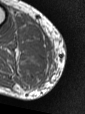
MRI of an extremity soft-tissue mass, one axial slice. Position 35 of 47 along the scan axis. MR volume resampled by the dataset authors to the PET/CT grid (not the native acquisition matrix). 3.27 mm slice thickness. 85 × 114 image matrix, field of view 83 × 111 mm. Male patient. From the clinical record (not read from this slice): histological type: pleiomorphic liposarcoma; grade: high; site of the primary tumour: right calf.
Annotated regions visible in this slice (expert contour drawn on MRI and transferred to this co-registered scan by the dataset authors):
- gross tumour volume including surrounding oedema: bounding box (x1, y1, x2, y2) in pixels: (40, 34, 52, 67)